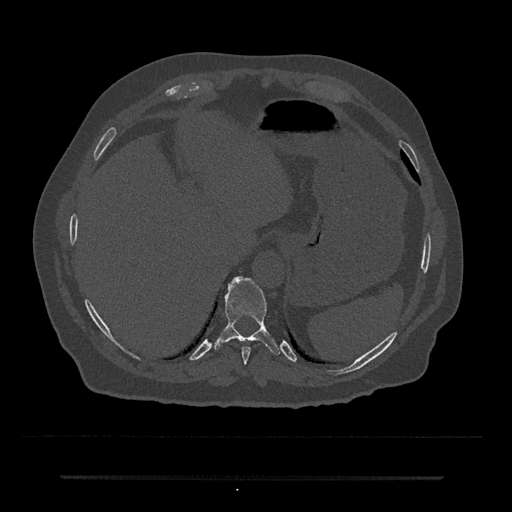
CT including the spine, one axial slice. Position 239 of 797 along the scan axis. Reconstruction kernel Br40s/3. 120 kVp. Bone window (W 1800 / L 400 HU). 0.5 mm slice thickness. 512 × 512 image matrix, field of view 437 × 437 mm. Male patient, age 69 years. Case-level facts recorded for this patient, not image findings: primary cancer: prostate.
Annotated regions visible in this slice (semi-automatically segmented with operator editing):
- T10 vertebra: bounding box <214,276,280,355> (left, top, right, bottom; pixels)
- T9 vertebra: <241,346,251,365>